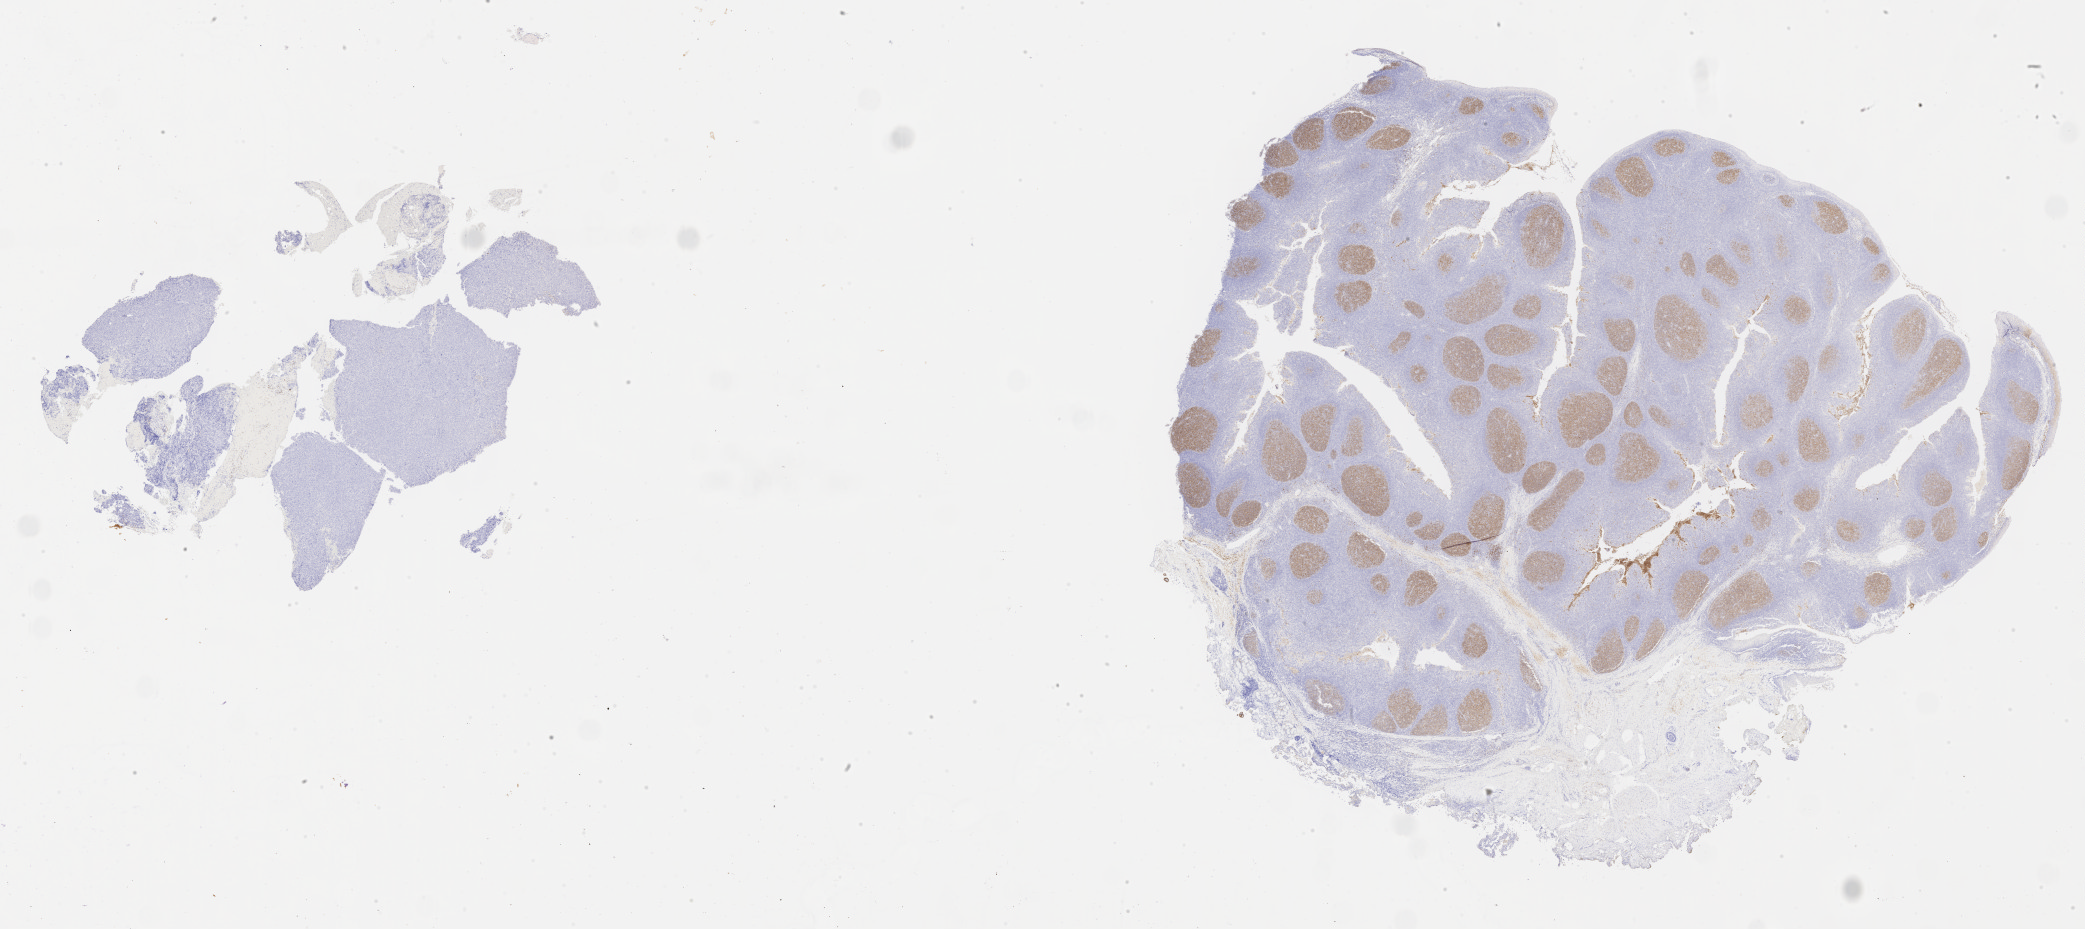
IHC for CD10, whole-slide image — shown as a low-resolution overview of the whole scanned area (about 33.7 x 15.0 mm). Tumor tissue. Anatomic site: lymph node. Patient: female, aged 71.
• histologic diagnosis: Diffuse large B-cell lymphoma, NOS